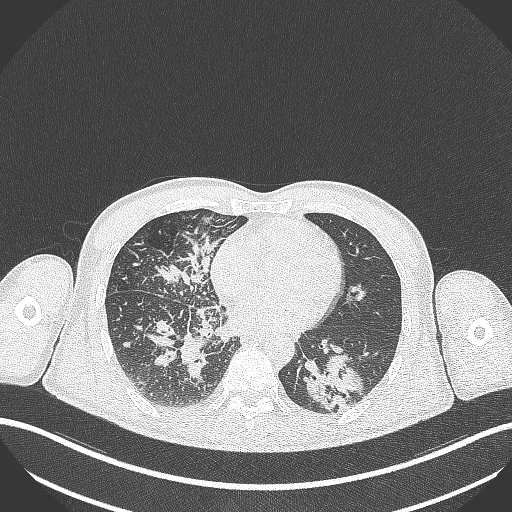
Chest CT, one axial slice; position 126 of 348 along the scan axis; reconstruction kernel B70f; lung window (W 1500 / L -600 HU); 512 × 512 image matrix. Male patient, age 49 years. From the clinical record (not read from this slice): clinical TNM (as recorded): T2b N1 M0.
Outlined on this slice (rectangle marked by the reading radiologist):
- lung tumour (recorded histology: adenocarcinoma): bounding box [x1, y1, x2, y2] px = [305, 356, 369, 412]